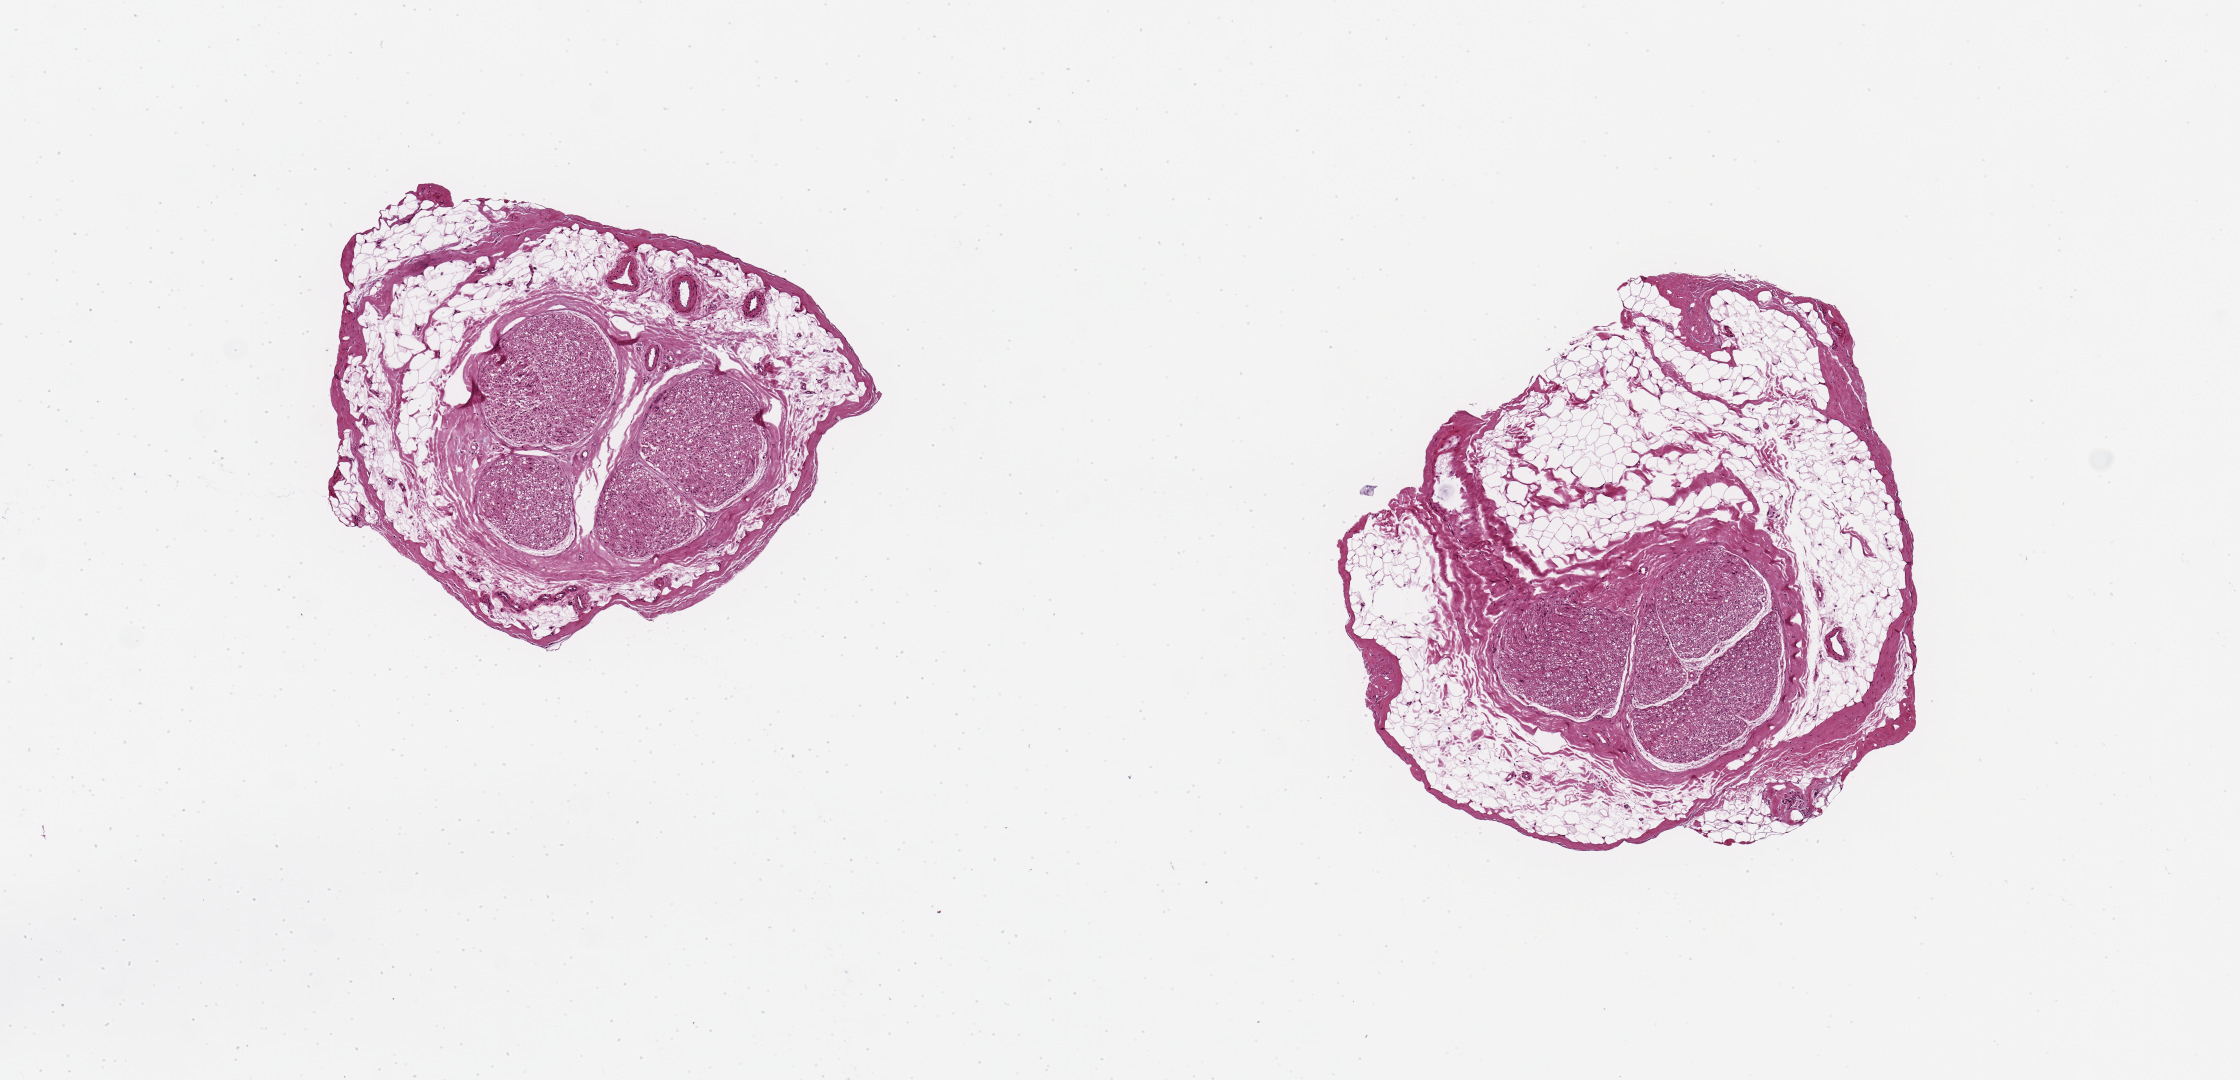
Whole-slide image, H&E stain, brightfield — a low-resolution overview of the entire scanned area, about 8.9 x 4.3 mm. PAXgene-fixed, paraffin-embedded tissue. Sampled site (target tissue): tibial nerve. Donor tissue sample. Donor: male.
Pathologist's review note for this sample: 2, 2mm pieces each with 1 mm nerves and 50-60% surrounding fat.